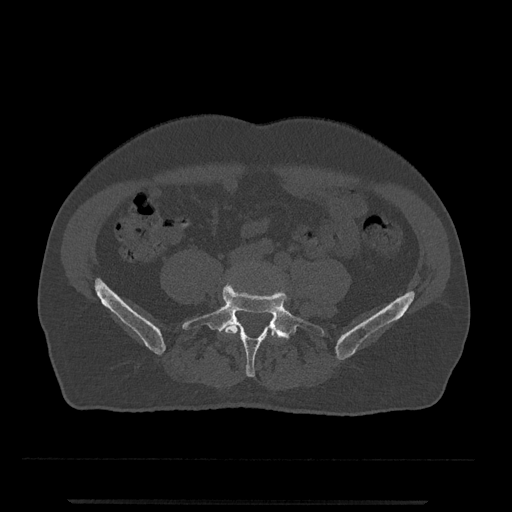
CT including the spine, one axial slice. Slice 87 of 797 in the series (ordered by position). Bone window (W 1800 / L 400 HU). 512 × 512 image matrix, field of view 419 × 419 mm. Patient: male, 63 years. From the clinical record (not read from this slice): primary cancer: prostate.
Structures marked on this image (semi-automatic segmentation, software-assisted and operator-edited):
- L4 vertebra: bounding box <223,320,277,340> (left, top, right, bottom; pixels)
- L5 vertebra: <182,283,325,377>